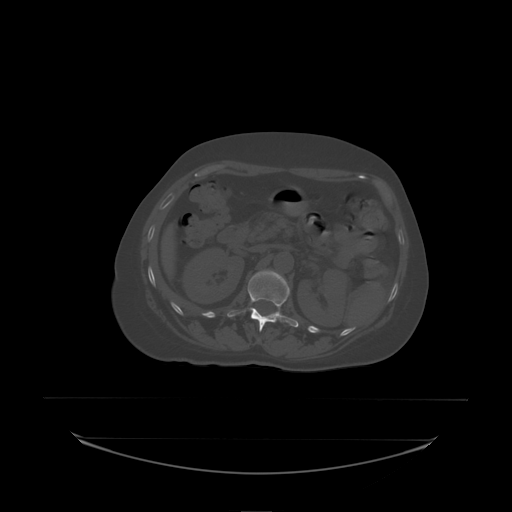
CT including the spine, one axial slice; slice 83 of 242 in the series (ordered by position); bone window (W 1800 / L 400 HU); 2.5 mm slice thickness; 512 × 512 image matrix, field of view 500 × 500 mm. Female patient, age 53 years. From the clinical record (not read from this slice): primary cancer: lung; vertebrae with lytic lesions (as recorded): T7, L1.
Structures marked on this image (semi-automatically segmented with operator editing):
- L1 vertebra: bounding box <228,270,299,332> (left, top, right, bottom; pixels)
- L2 vertebra: <261,270,265,272>